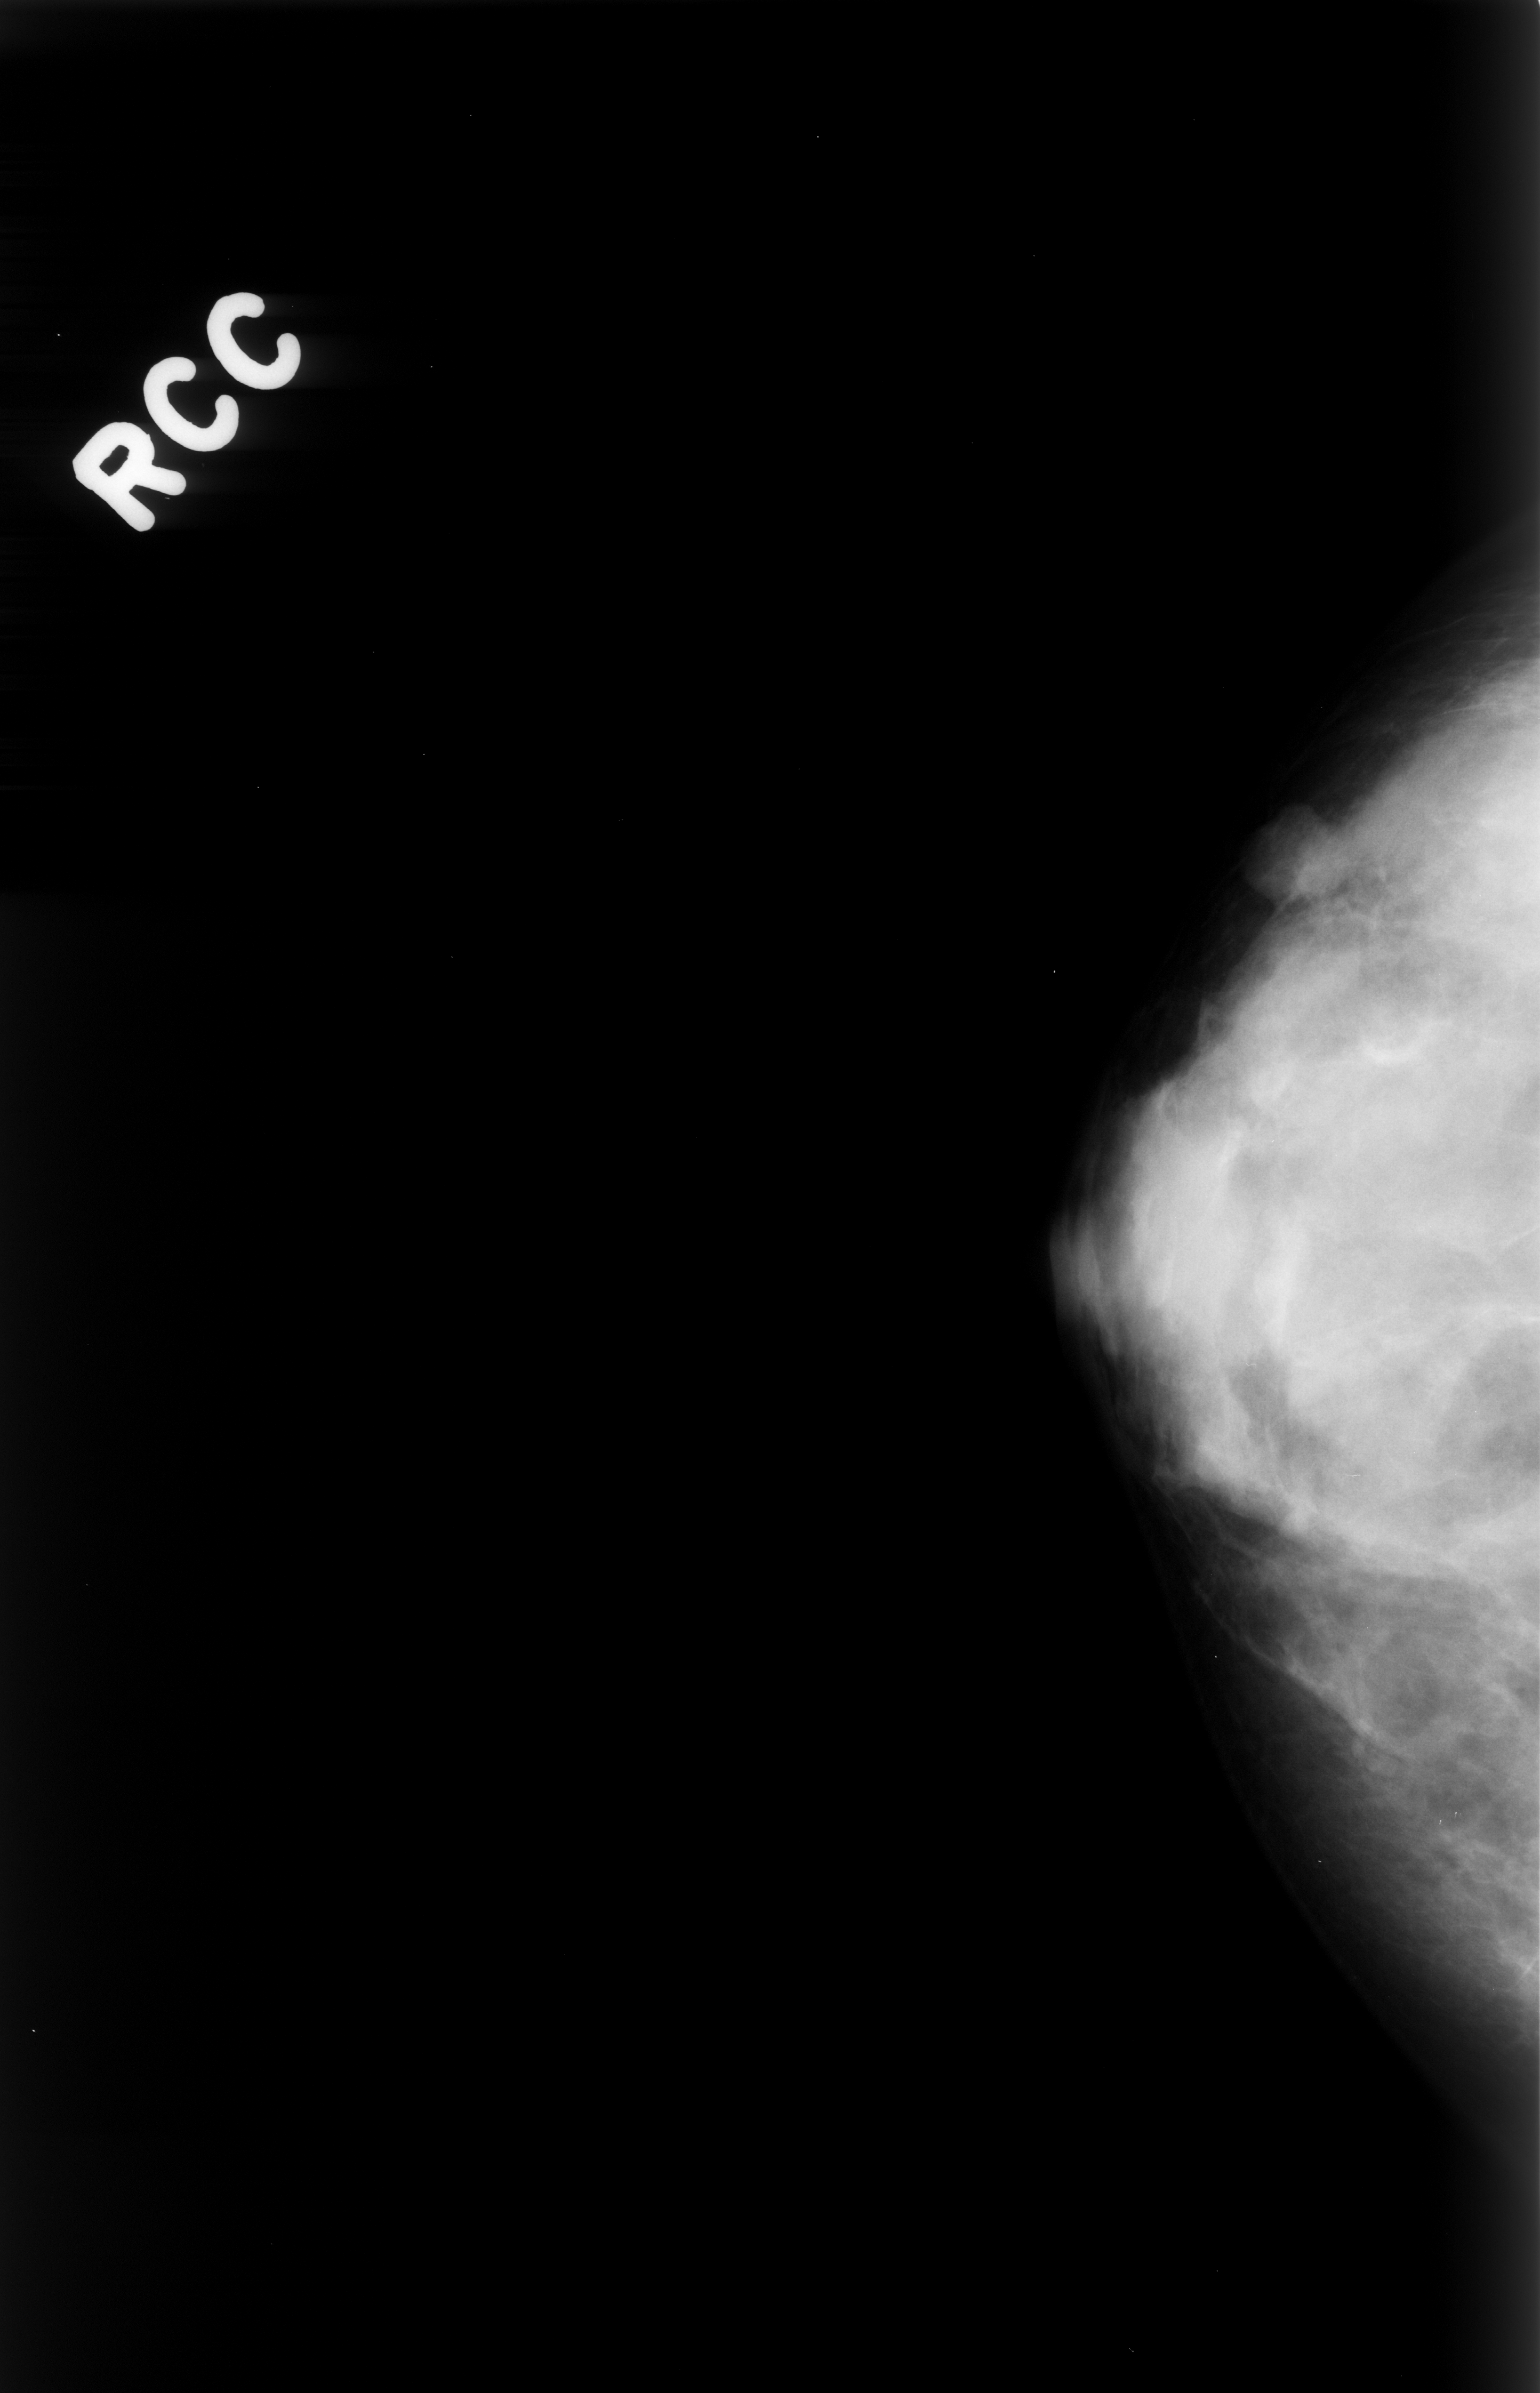
Scanned film-screen mammogram, right breast, CC view, breast composition: heterogeneously dense (BI-RADS density category 3 of 4).
Abnormality record for this image: mass, shape oval, margins circumscribed; BI-RADS assessment category 4; pathology result (as recorded, not read from the image): benign.